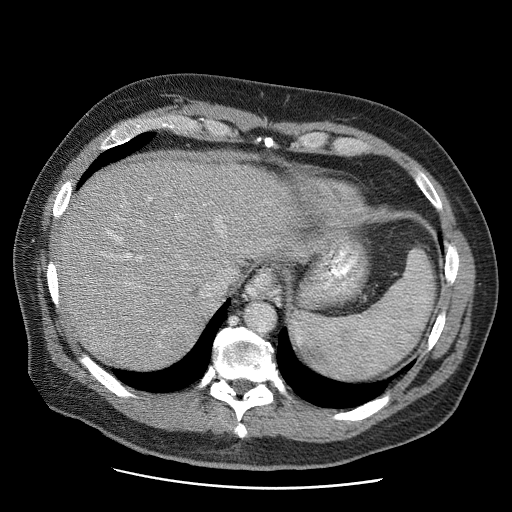
Contrast-enhanced abdominal CT (liver protocol), one axial slice; slice 47 of 81 in the series (ordered by position); 120 kVp; soft-tissue window (W 400 / L 40 HU); 512 × 512 image matrix, field of view 380 × 380 mm. From the clinical record (not read from this slice): diagnosis: hepatocellular carcinoma (patient treated with transarterial chemoembolisation; whether this scan precedes or follows treatment is not stated here); TNM stage (as recorded): Stage-IIIA; Child-Pugh class: A; tumour differentiation: moderately differentiated; tumour nodularity: multinodular.
Structures marked on this image (semi-automatic segmentation, software-assisted and operator-edited):
- liver parenchyma outside the tumour (the mass and vessels are separate outlines, so this box may not span the whole liver): bounding box (x1, y1, x2, y2) in pixels: (56, 156, 340, 368)
- liver vessels: (117, 197, 152, 259)